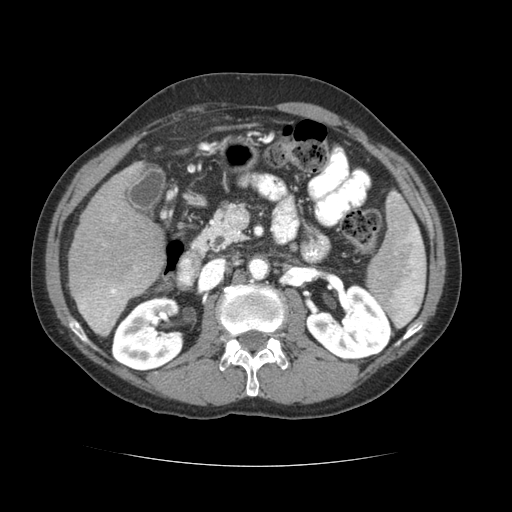
Contrast-enhanced abdominal CT (liver protocol), one axial slice; slice 28 of 69 in the series (ordered by position); reconstruction kernel STANDARD; 120 kVp; soft-tissue window (W 400 / L 40 HU); 2.5 mm slice thickness; 512 × 512 image matrix. Case-level facts recorded for this patient, not image findings: diagnosis: hepatocellular carcinoma (patient treated with transarterial chemoembolisation; whether this scan precedes or follows treatment is not stated here); TNM stage (as recorded): Stage-II; Child-Pugh class: B; tumour nodularity: multinodular; tumour size: 2.6 cm.
Structures marked on this image (semi-automatically segmented with operator editing):
- liver parenchyma outside the tumour (the mass and vessels are separate outlines, so this box may not span the whole liver): bounding box [x1, y1, x2, y2] px = [68, 162, 164, 334]
- liver vessels: [79, 219, 140, 331]